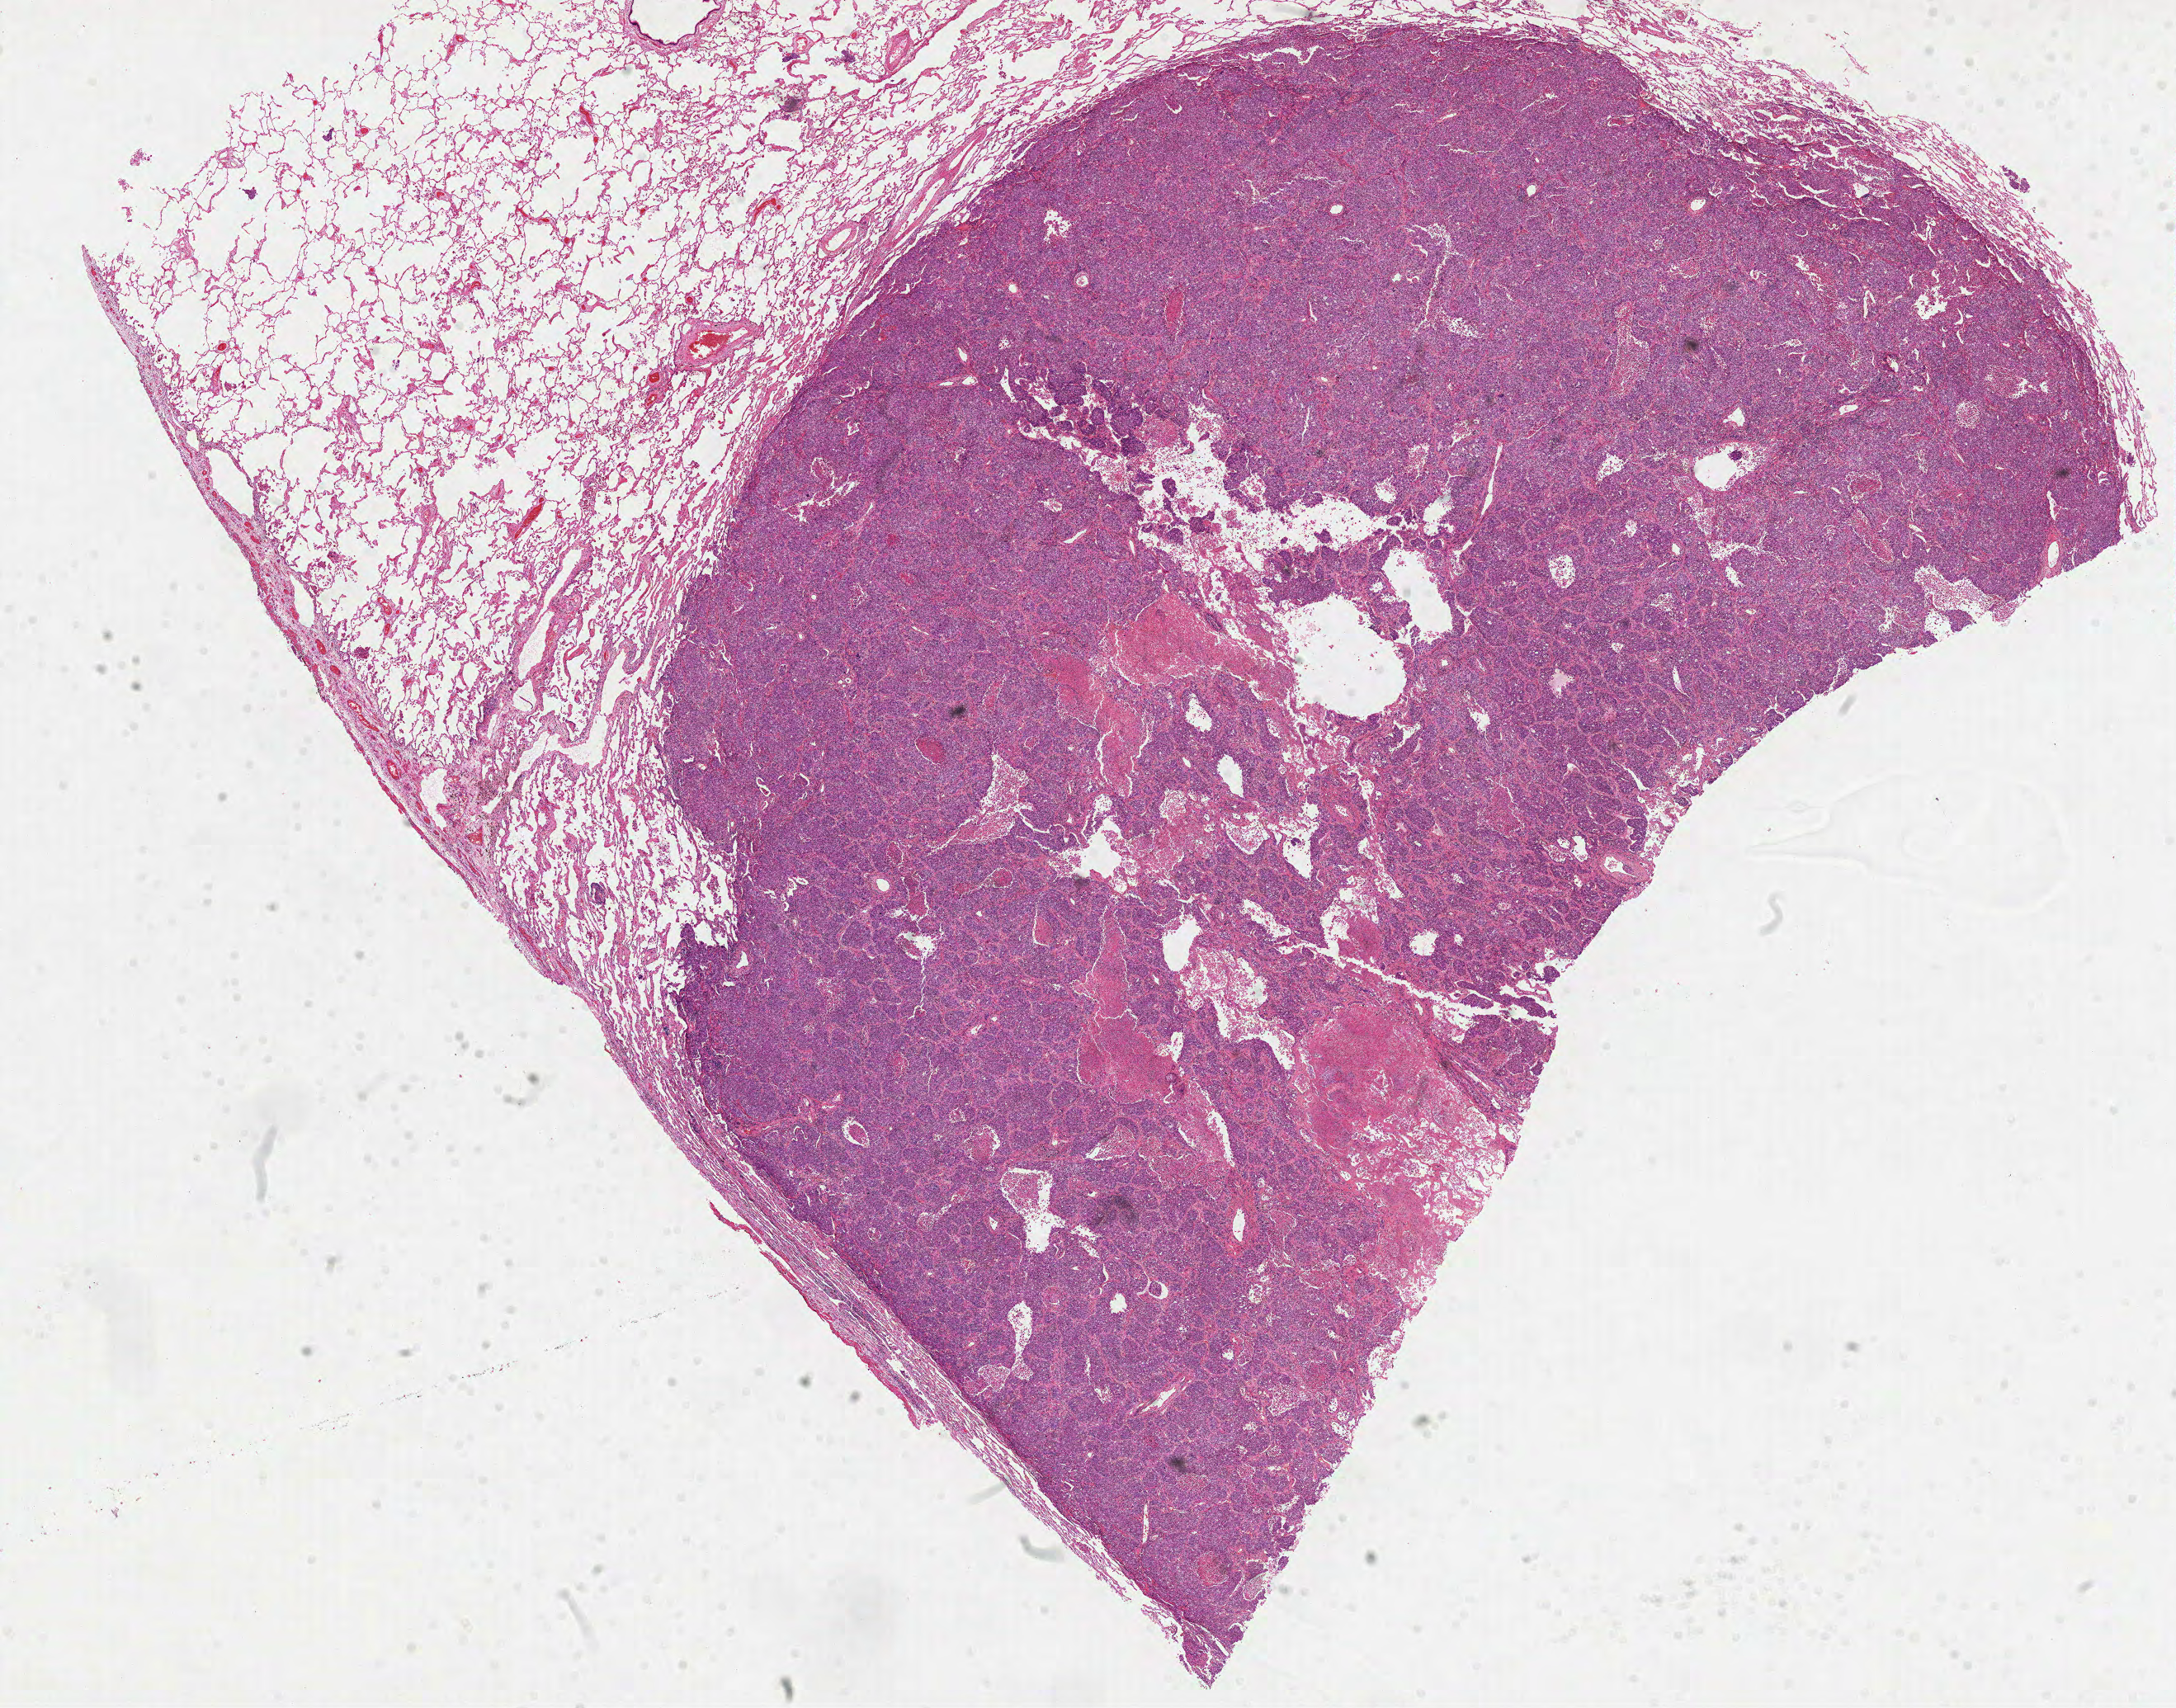
Whole-slide histology image, Hematoxylin and eosin (H&E) stained — whole scanned area (about 21.3 x 16.7 mm) shown as a low-resolution overview; formalin-fixed paraffin-embedded (FFPE) diagnostic section; sample: primary tumour, lung. Female, age 71 years at initial diagnosis.
* AJCC pathologic stage: IIIA (6th edition)
* TNM: T2 N2 M0
* pathologic diagnosis: Adenocarcinoma with mixed subtypes (lower lobe, lung)
* laterality: left